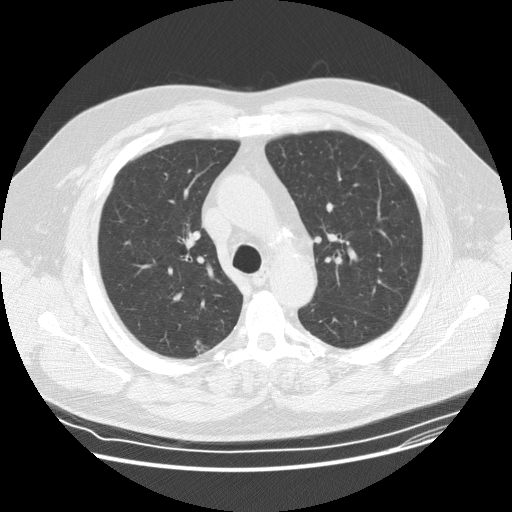
Chest CT (low-dose screening protocol), one axial image; baseline annual screen; lung window (W 1500 / L -600 HU). Male participant, aged 62 years at enrolment. Former smoker at enrolment.
Expert-annotated lung lesion, bounding box <180,331,218,368> (left, top, right, bottom; pixels). Screening reader's record for this exam (one nodule recorded; not confirmed to be the boxed lesion): non-calcified nodule or mass ≥4 mm, right upper lobe, 8 × 7 mm, smooth margins, ground glass attenuation. Later outcome: lung cancer diagnosed 795 days after this screen — bronchiolo-alveolar adenocarcinoma, NOS, right upper lobe, well differentiated (G1), stage IA (AJCC 6th edition), 12 mm at pathology.